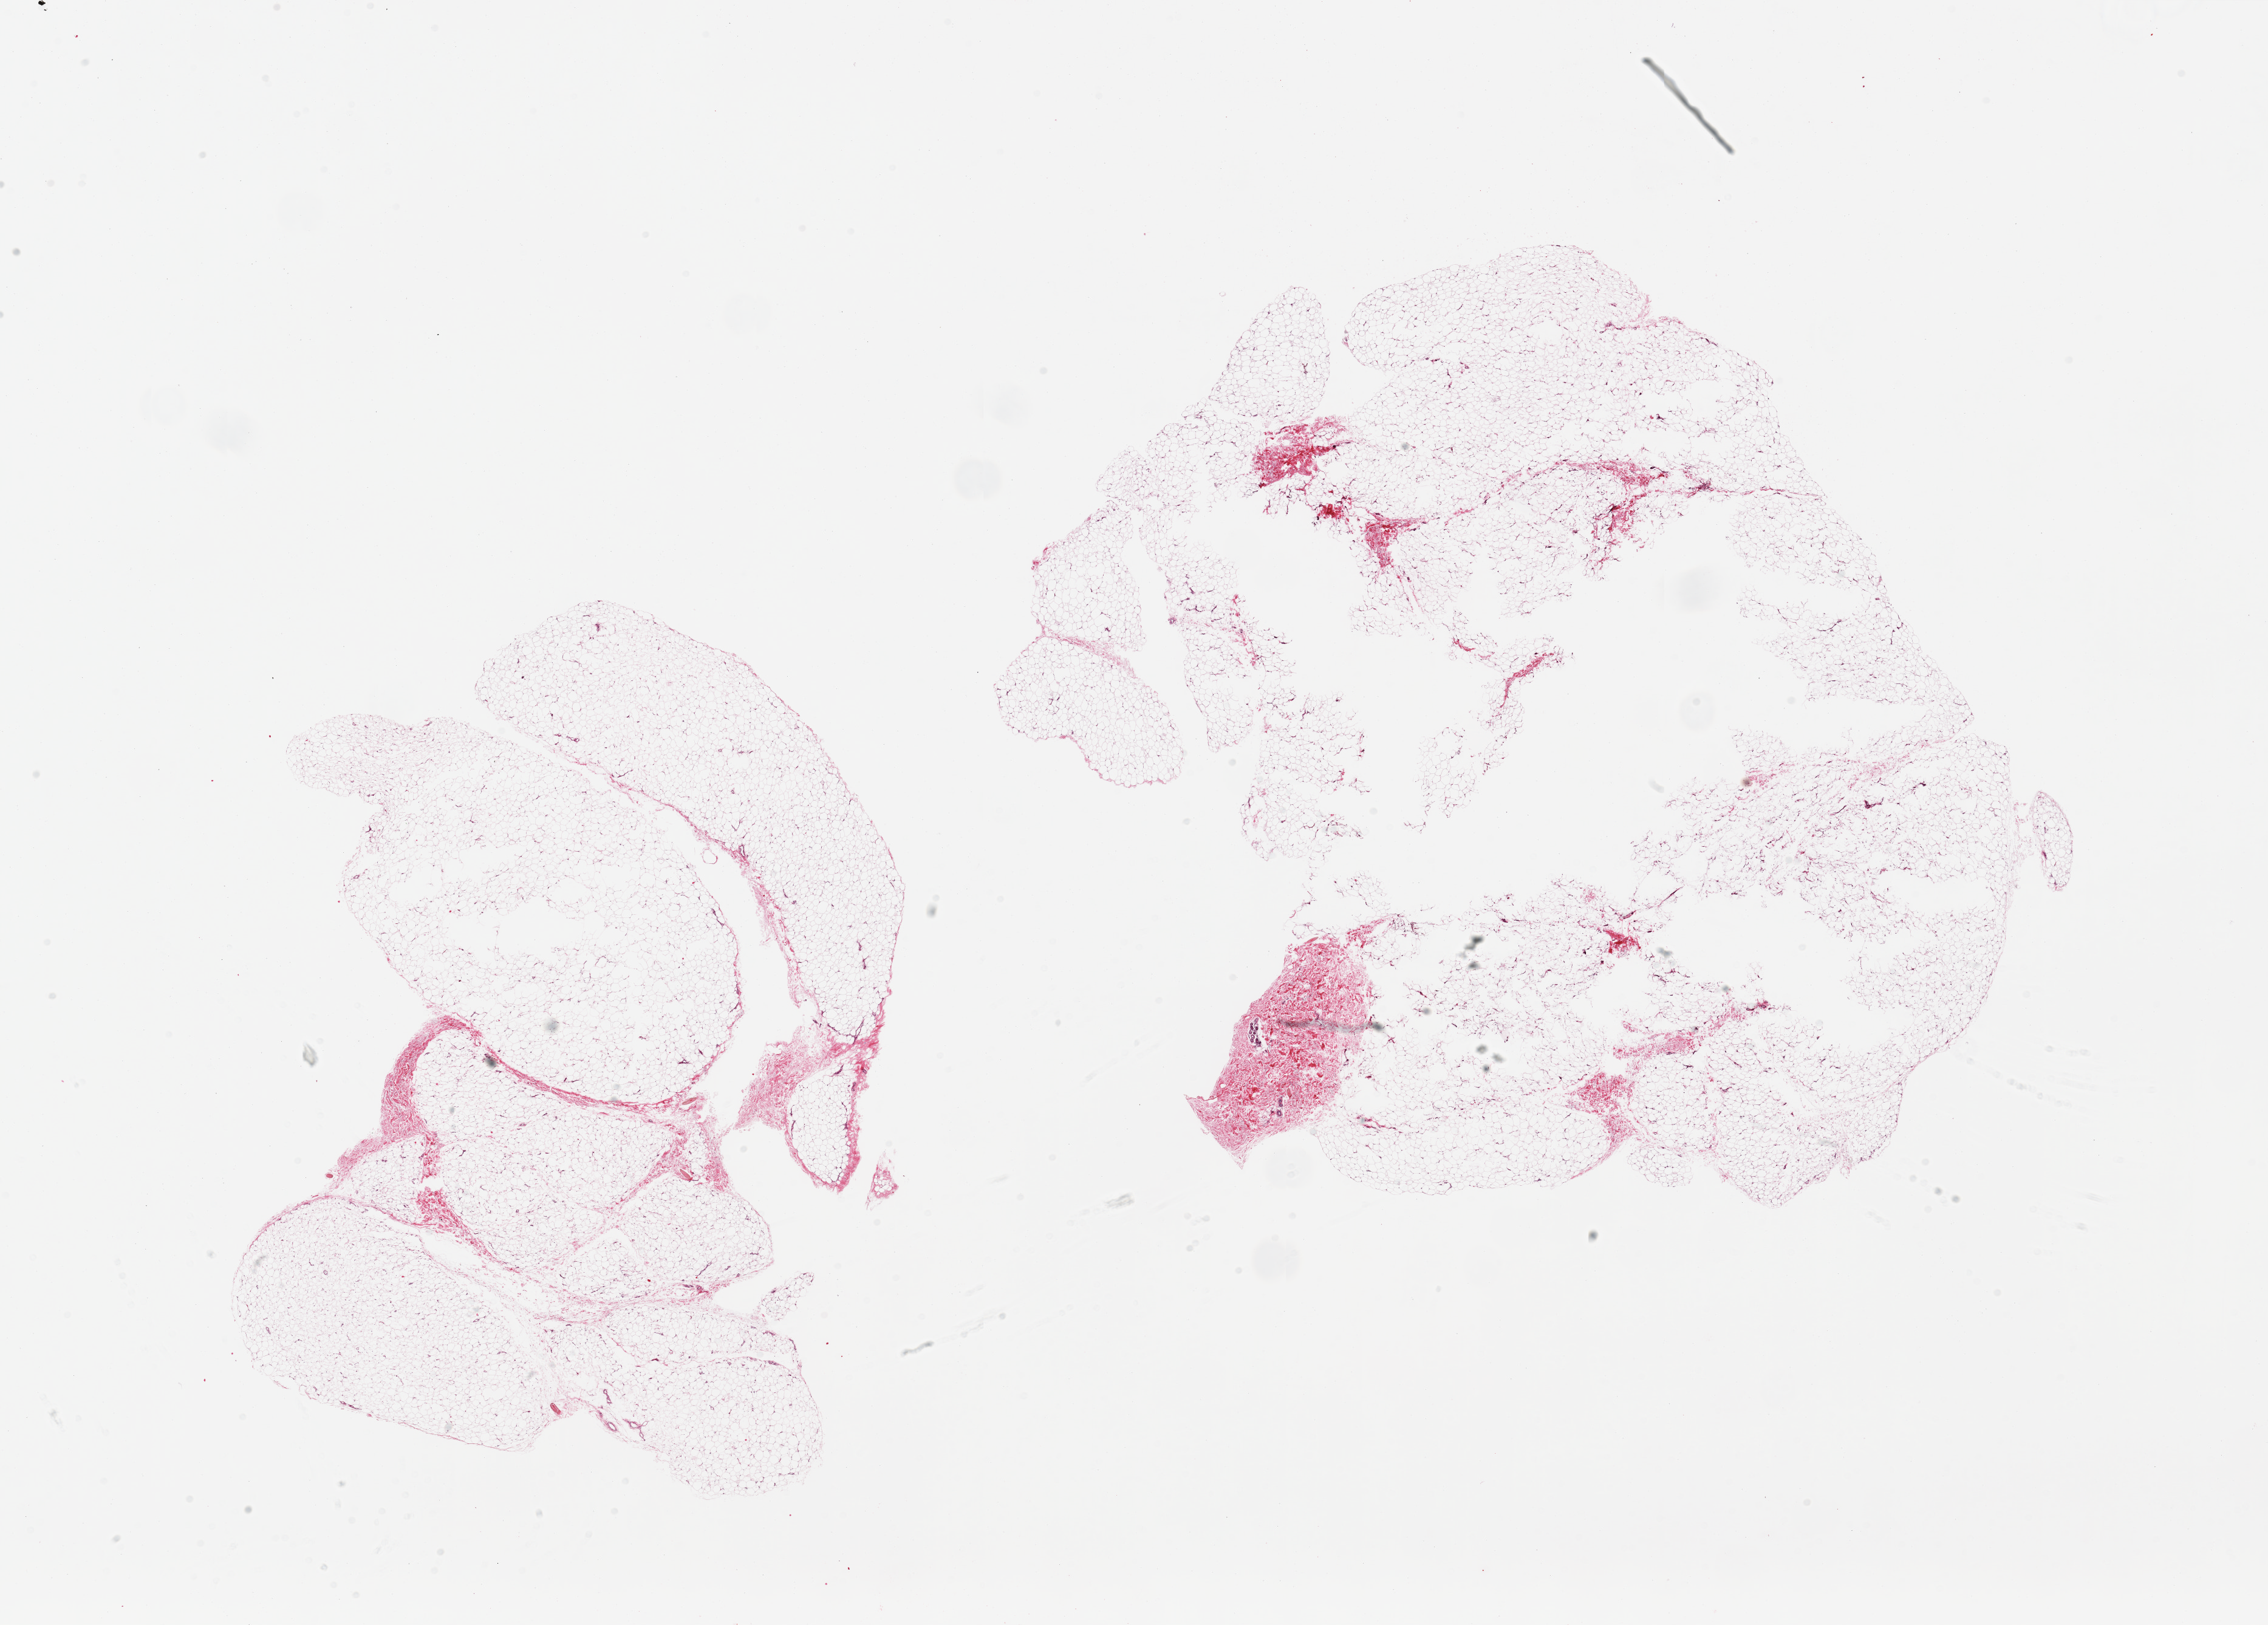
H&E whole-slide image, shown as a low-resolution overview of the whole scanned area (about 29.5 x 21.2 mm, acquisition: 20x scan). PAXgene-fixed, paraffin-embedded tissue. Sampled site (target tissue): adipose tissue. Tissue donor sample. Donor: male.
- pathologist's review note for this sample: 2 pieces; over-sized and with central defects (?poor fixation), few sweat glands